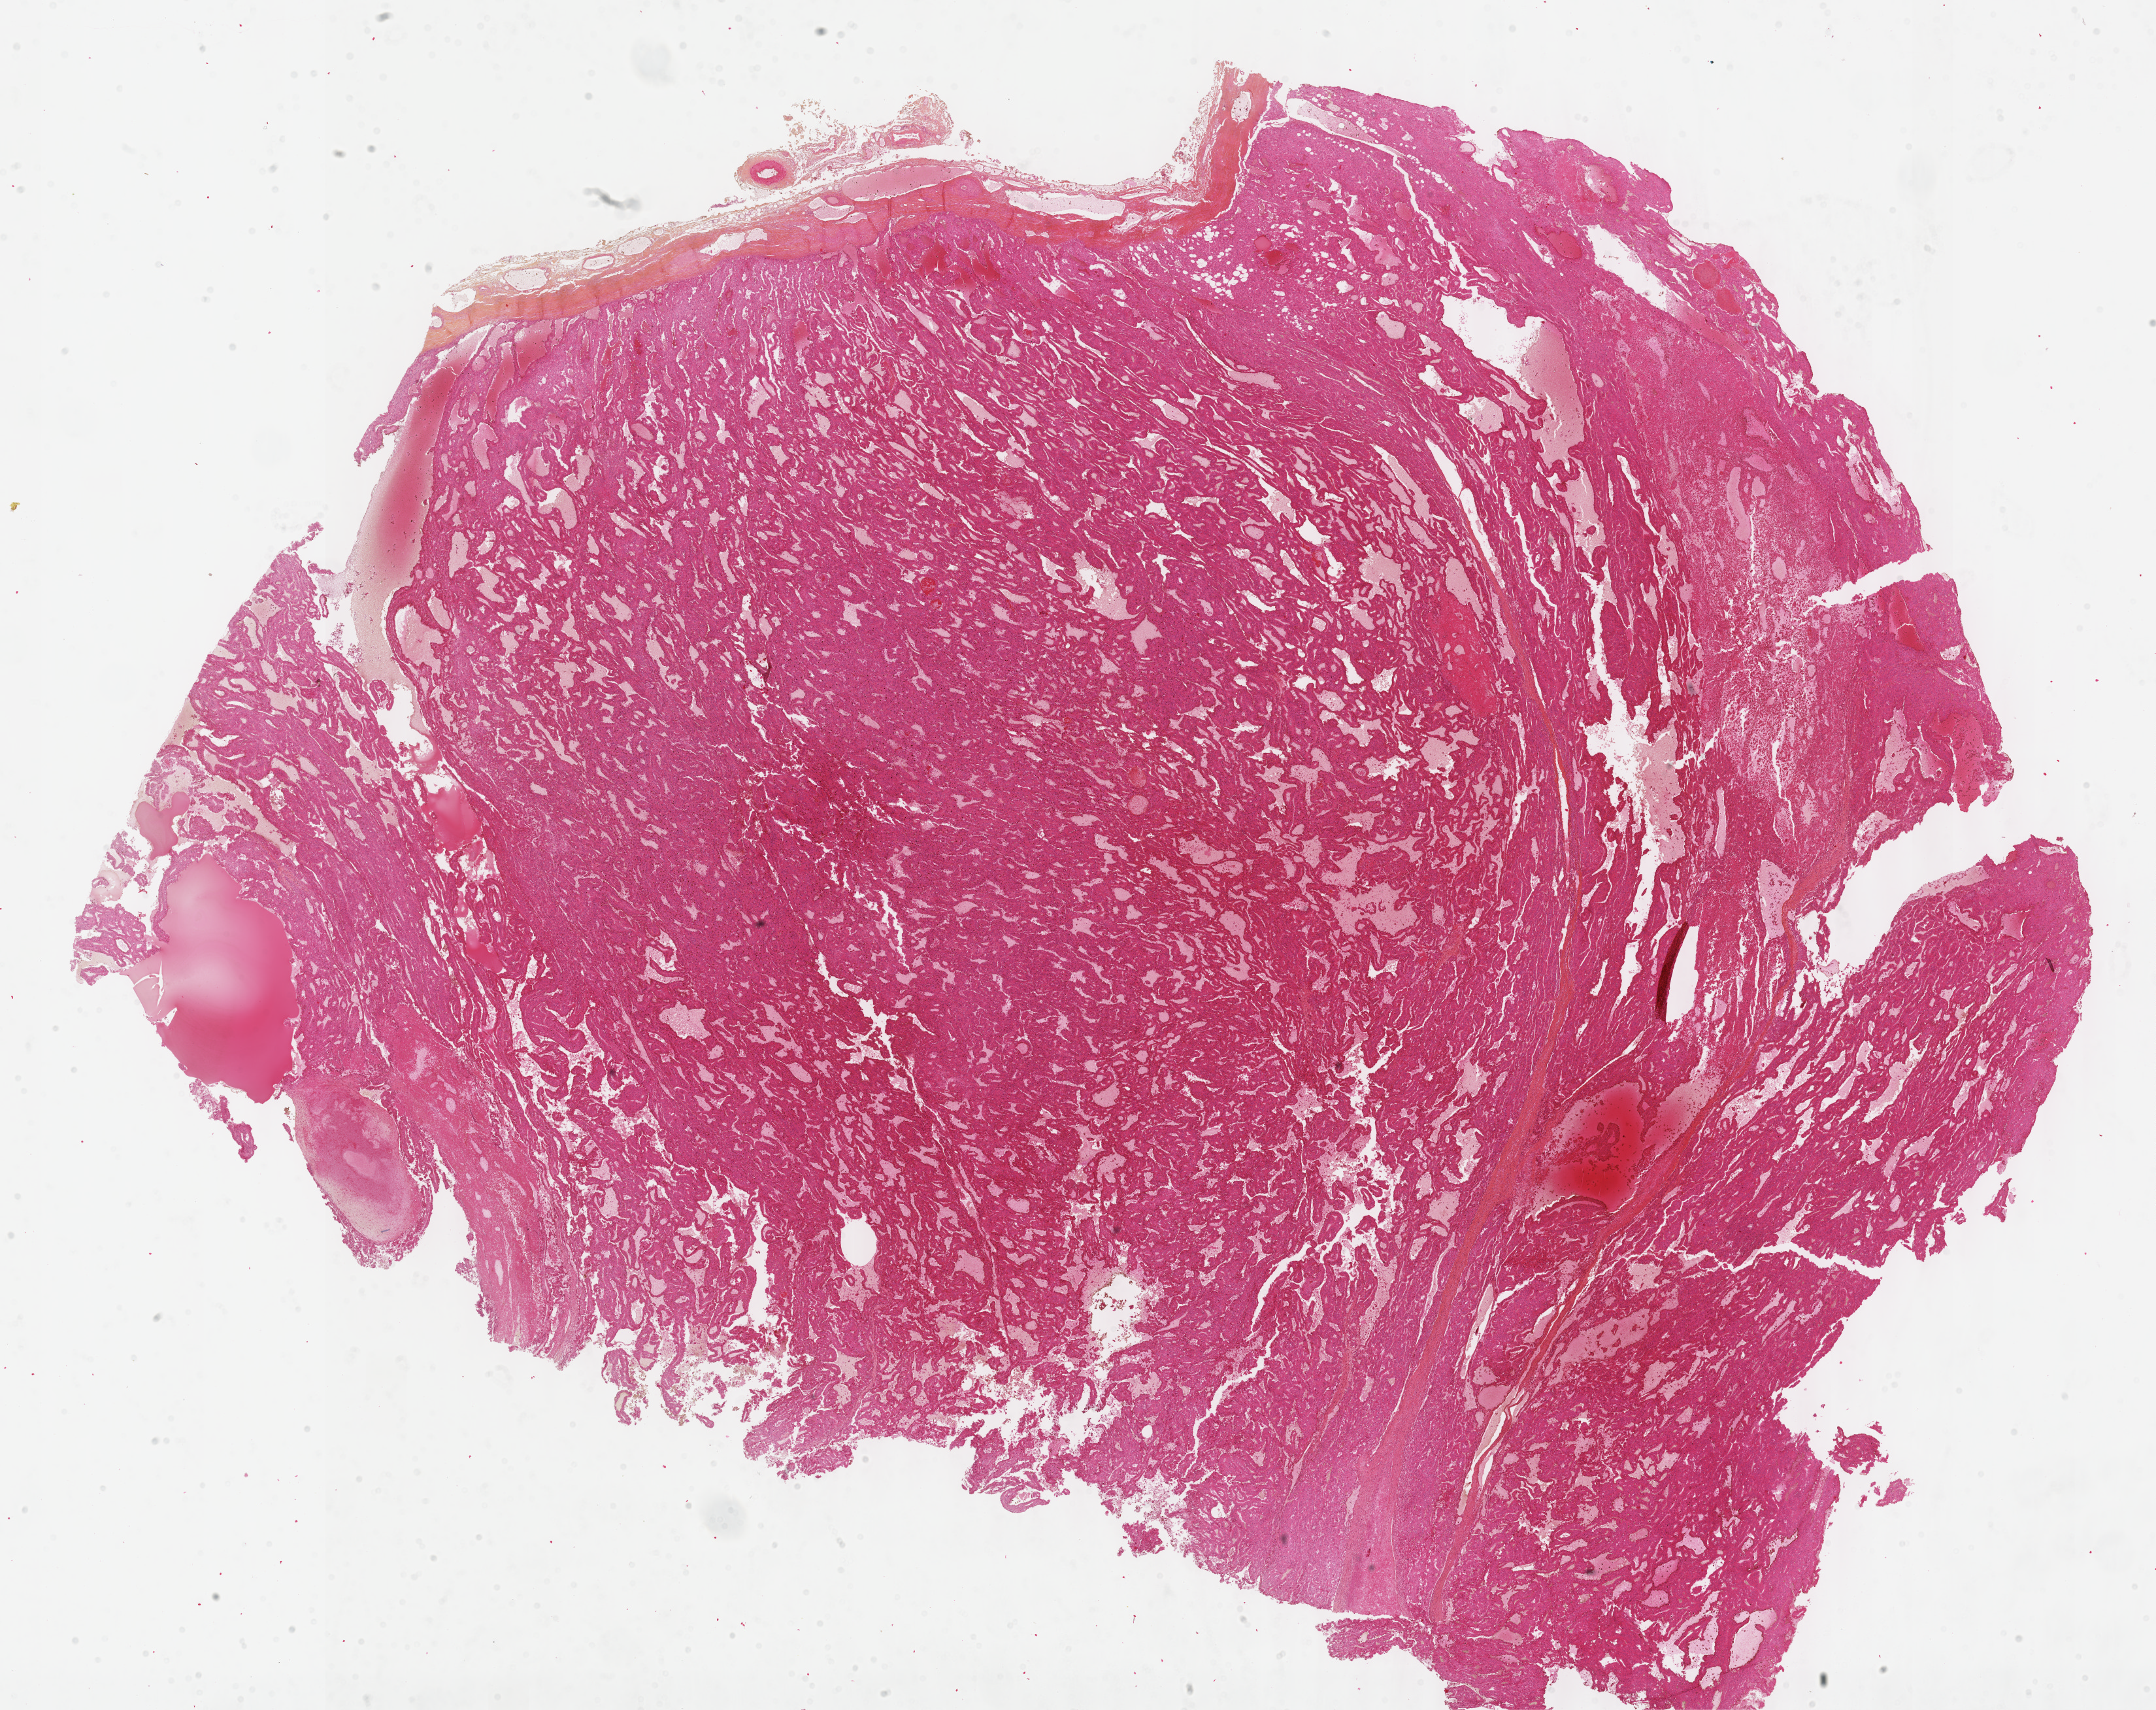
H&E-stained whole-slide image — low-resolution overview of the scanned area, about 26.7 x 21.1 mm (acquisition: 40x scan); formalin-fixed paraffin-embedded (FFPE) diagnostic section; sample: primary tumour, adrenal cortex. Female patient; age at initial diagnosis 34 years.
Diagnosis: Adrenal cortical carcinoma (cortex of adrenal gland).